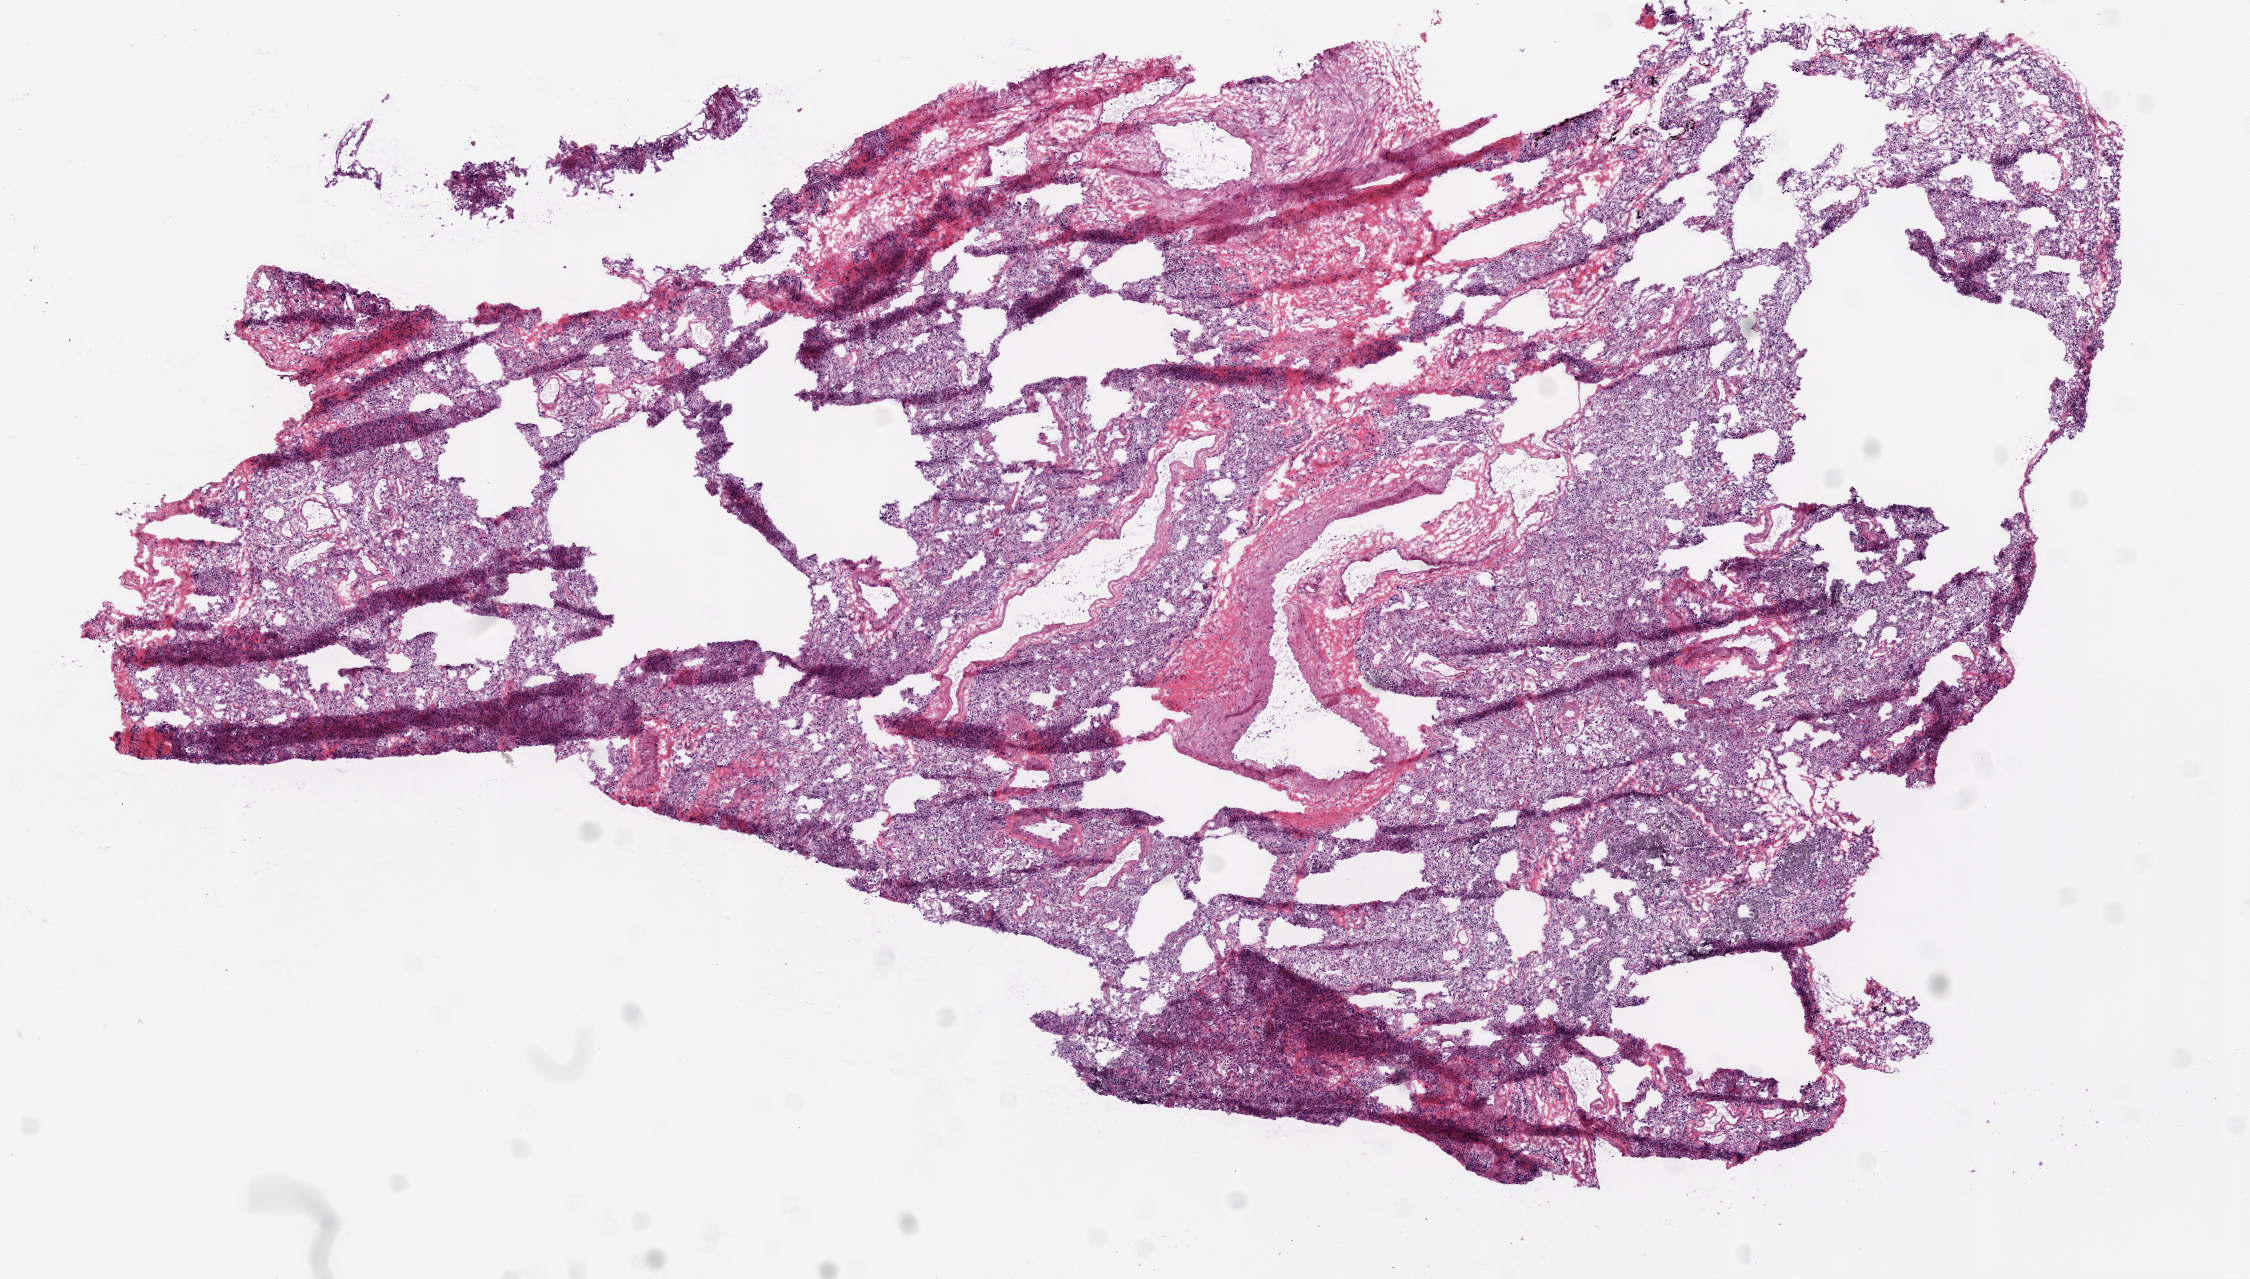
H&E-stained whole-slide image, a low-resolution overview of the entire scanned area, about 9.0 x 5.1 mm; frozen section from the bottom of the tissue portion; solid tissue normal (non-tumour tissue) sample from the lung. Patient: female, age at initial diagnosis 68 years.
This section: solid tissue normal (non-tumour) sample from the same patient. Patient diagnosis: Squamous cell carcinoma, NOS (upper lobe, lung).